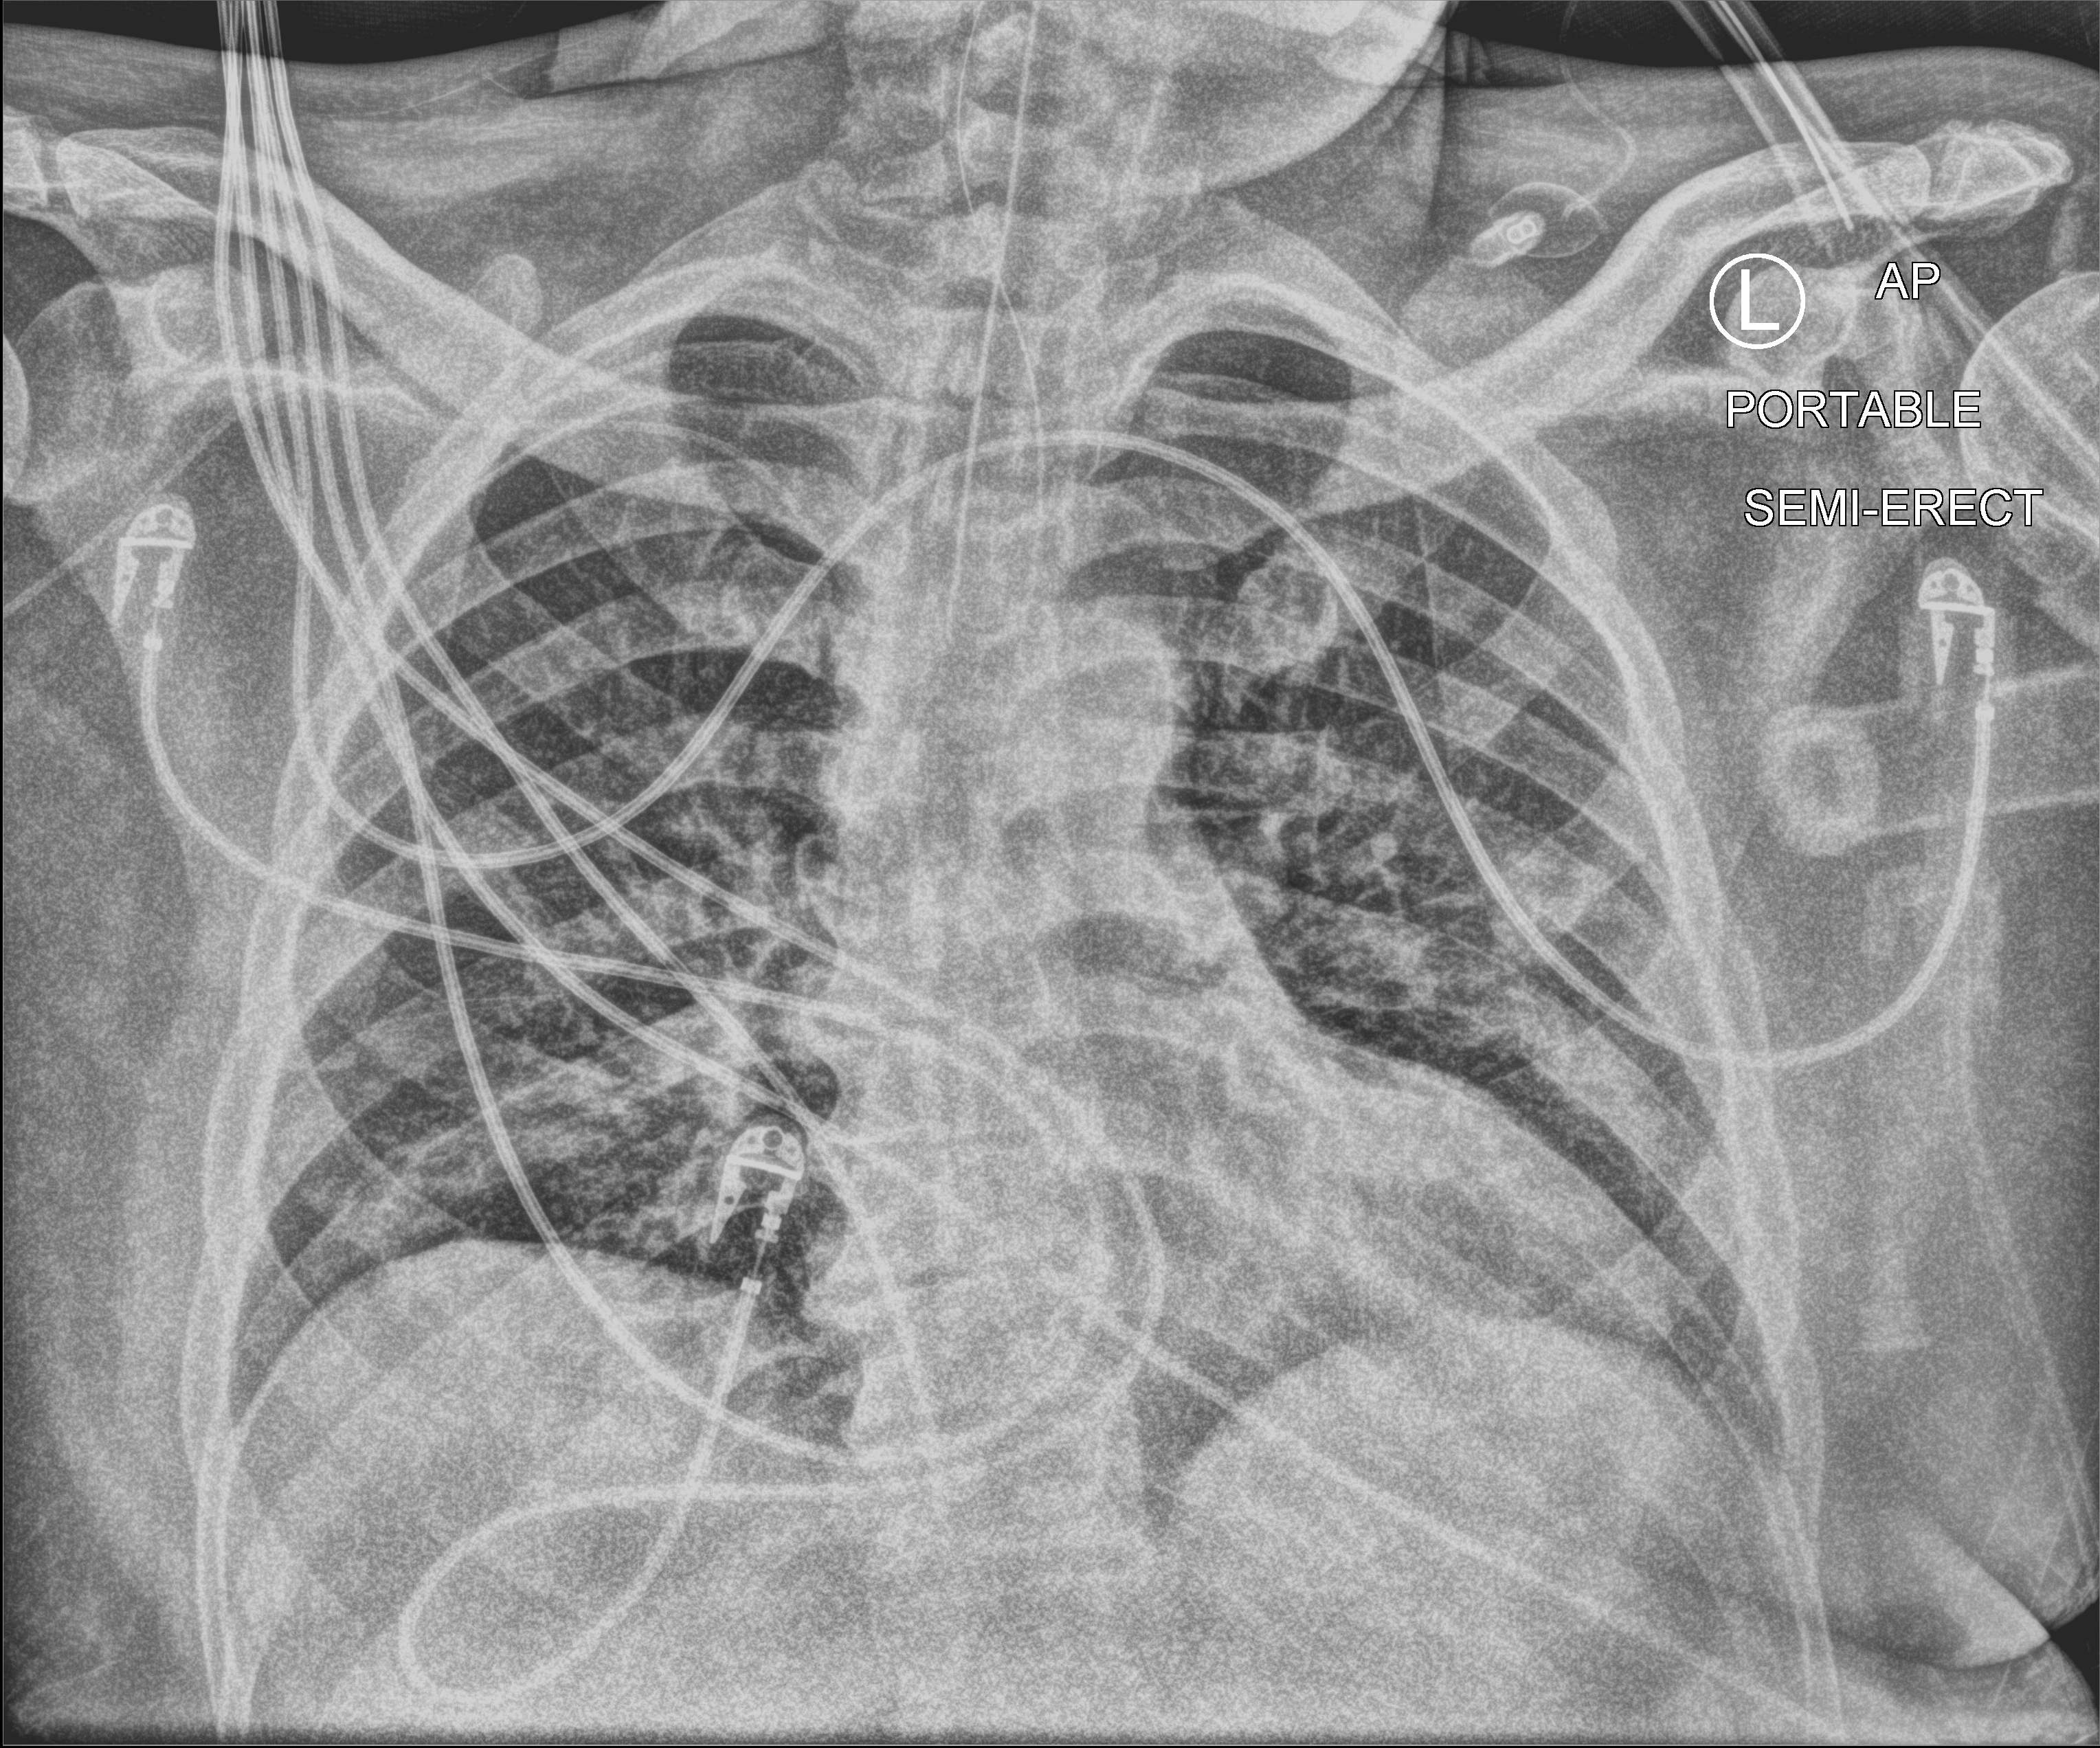
Bedside chest radiograph (computed radiography); anteroposterior (AP) projection. Male patient hospitalised with COVID-19, age 18–59 years.
Hospital-stay facts (about this admission, not read from this image; timing relative to this image not recorded): chronic kidney disease (admission record): no; mechanically ventilated during this hospital stay: yes; length of hospital stay: 41 days.